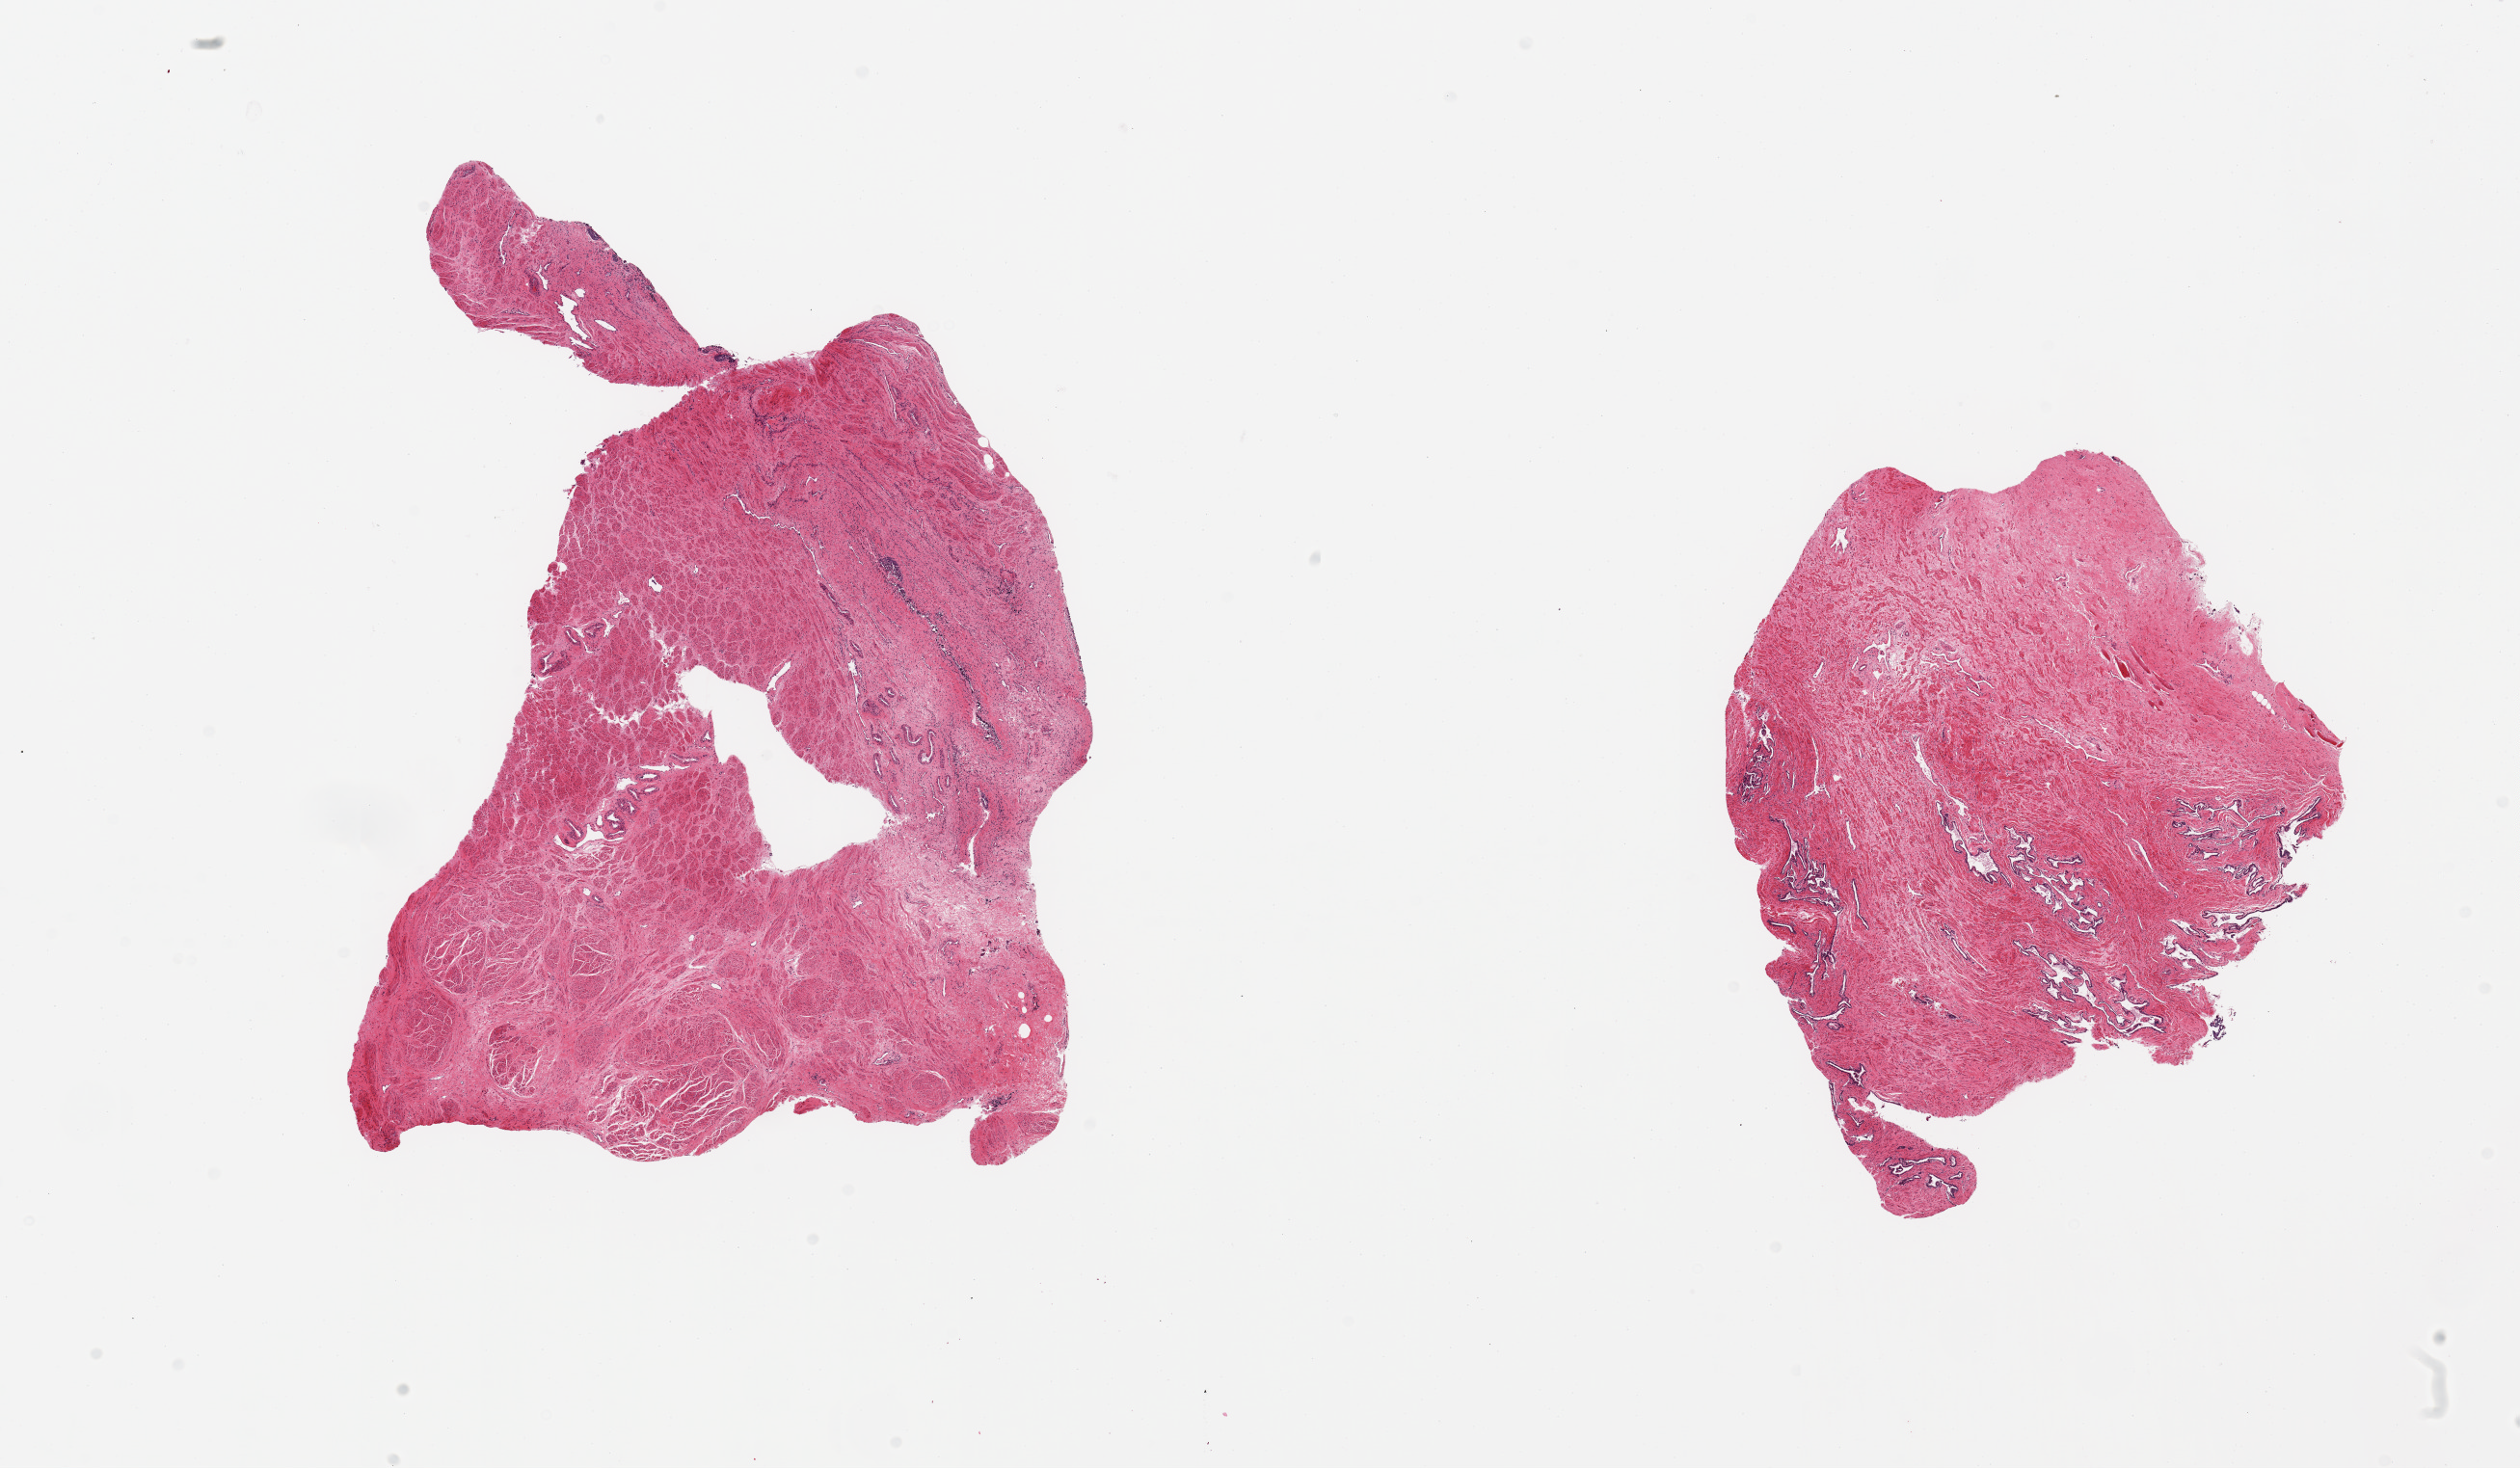
Digitized hematoxylin and eosin (H&E)-stained section, brightfield — low-resolution overview of the scanned area, about 20.7 x 12.0 mm, PAXgene-fixed paraffin-embedded (PFPE) section, section of prostate (target tissue), donor tissue sample. Male donor.
Reviewer comment on this tissue sample: 2 pieces; mostly fibromuscular stroma, few glands.